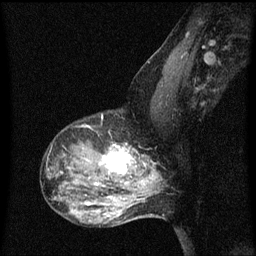
Breast MRI (dynamic contrast-enhanced), one sagittal slice. Slice 41 of 60 in the series (ordered by position). Dynamic contrast-enhanced series, image 2 of 3 at this slice position (ordered by acquisition). 1.5 T. TE 4.2 ms, TR 8 ms. 2 mm slice thickness. 256 × 256 image matrix, field of view 200 × 200 mm. Female patient, age 50 years.
Structures marked on this image (semi-automatic segmentation, software-assisted and operator-edited):
- analysis volume of interest (the breast-tissue region the enhancement analysis was run in; not a lesion): box from (x=91, y=142) to (x=141, y=189) px
- tumour enhancement mask (voxels above the 70 % enhancement threshold inside the analysis volume of interest): (x=95, y=146)–(x=133, y=185)